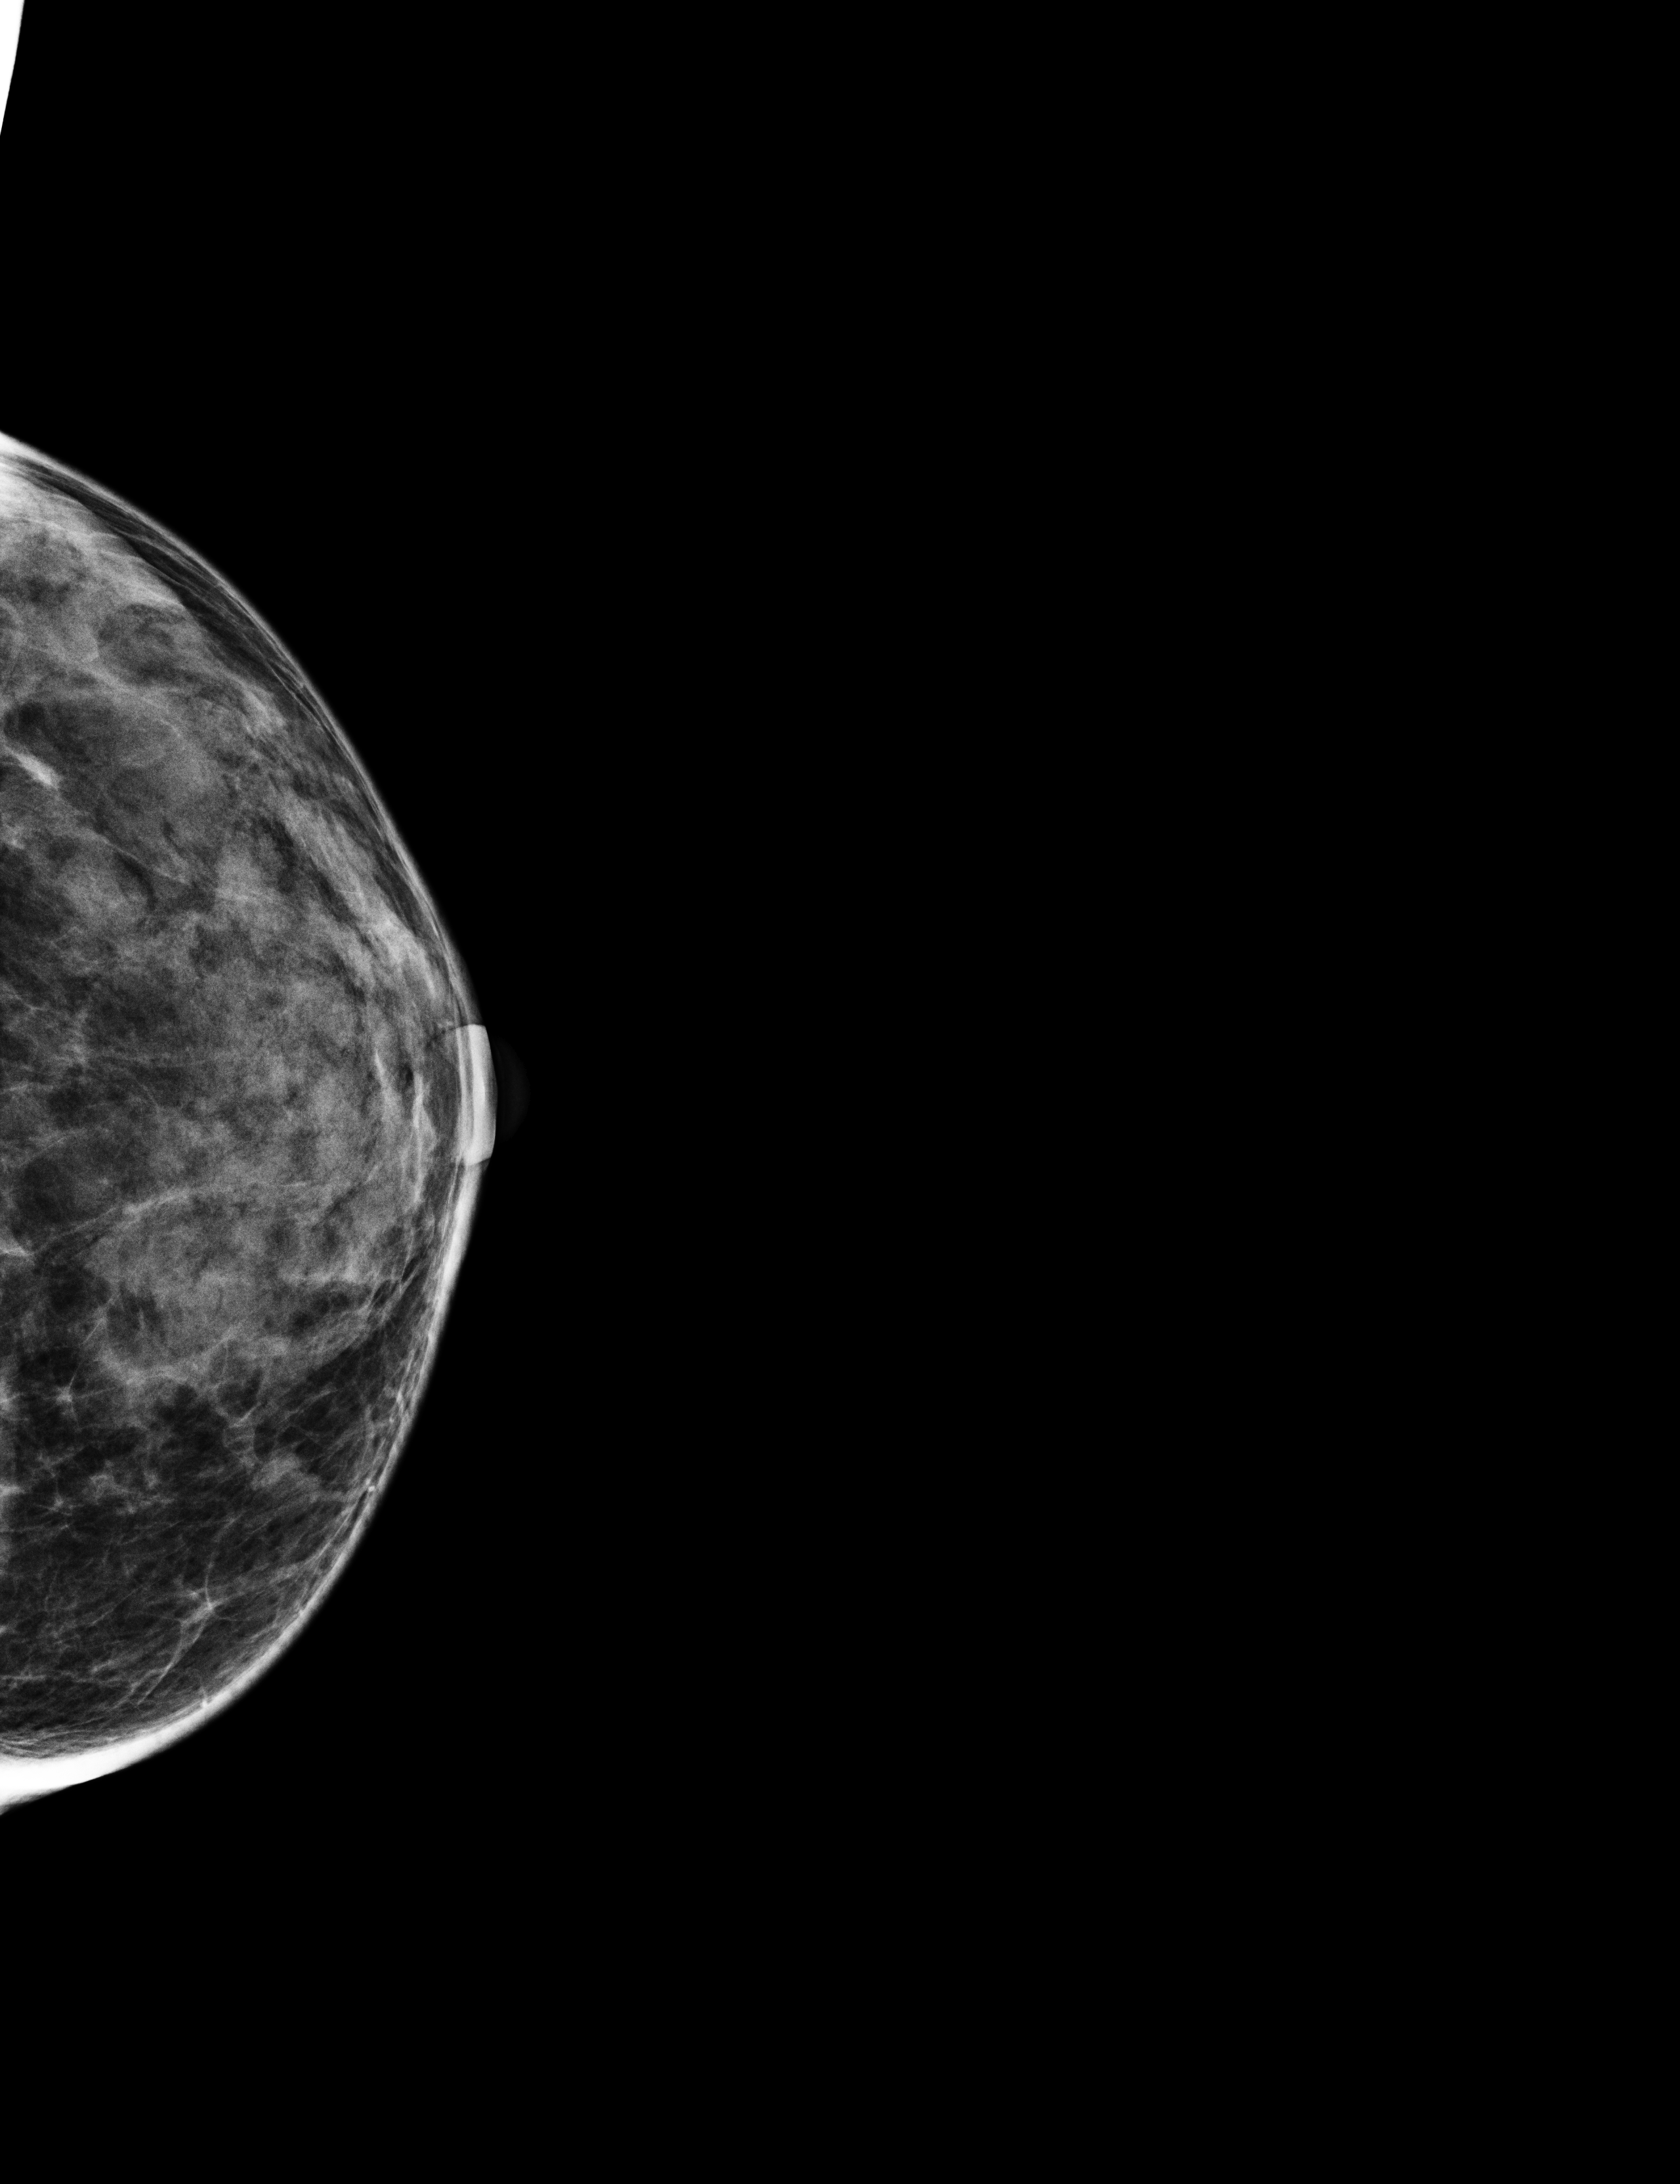
Screening examination; compressed breast thickness 27 mm; system: Selenia Dimensions. Patient aged 44 years (female).
Image type: full-field digital mammogram. Breast: left. Projection: cranio-caudal projection.